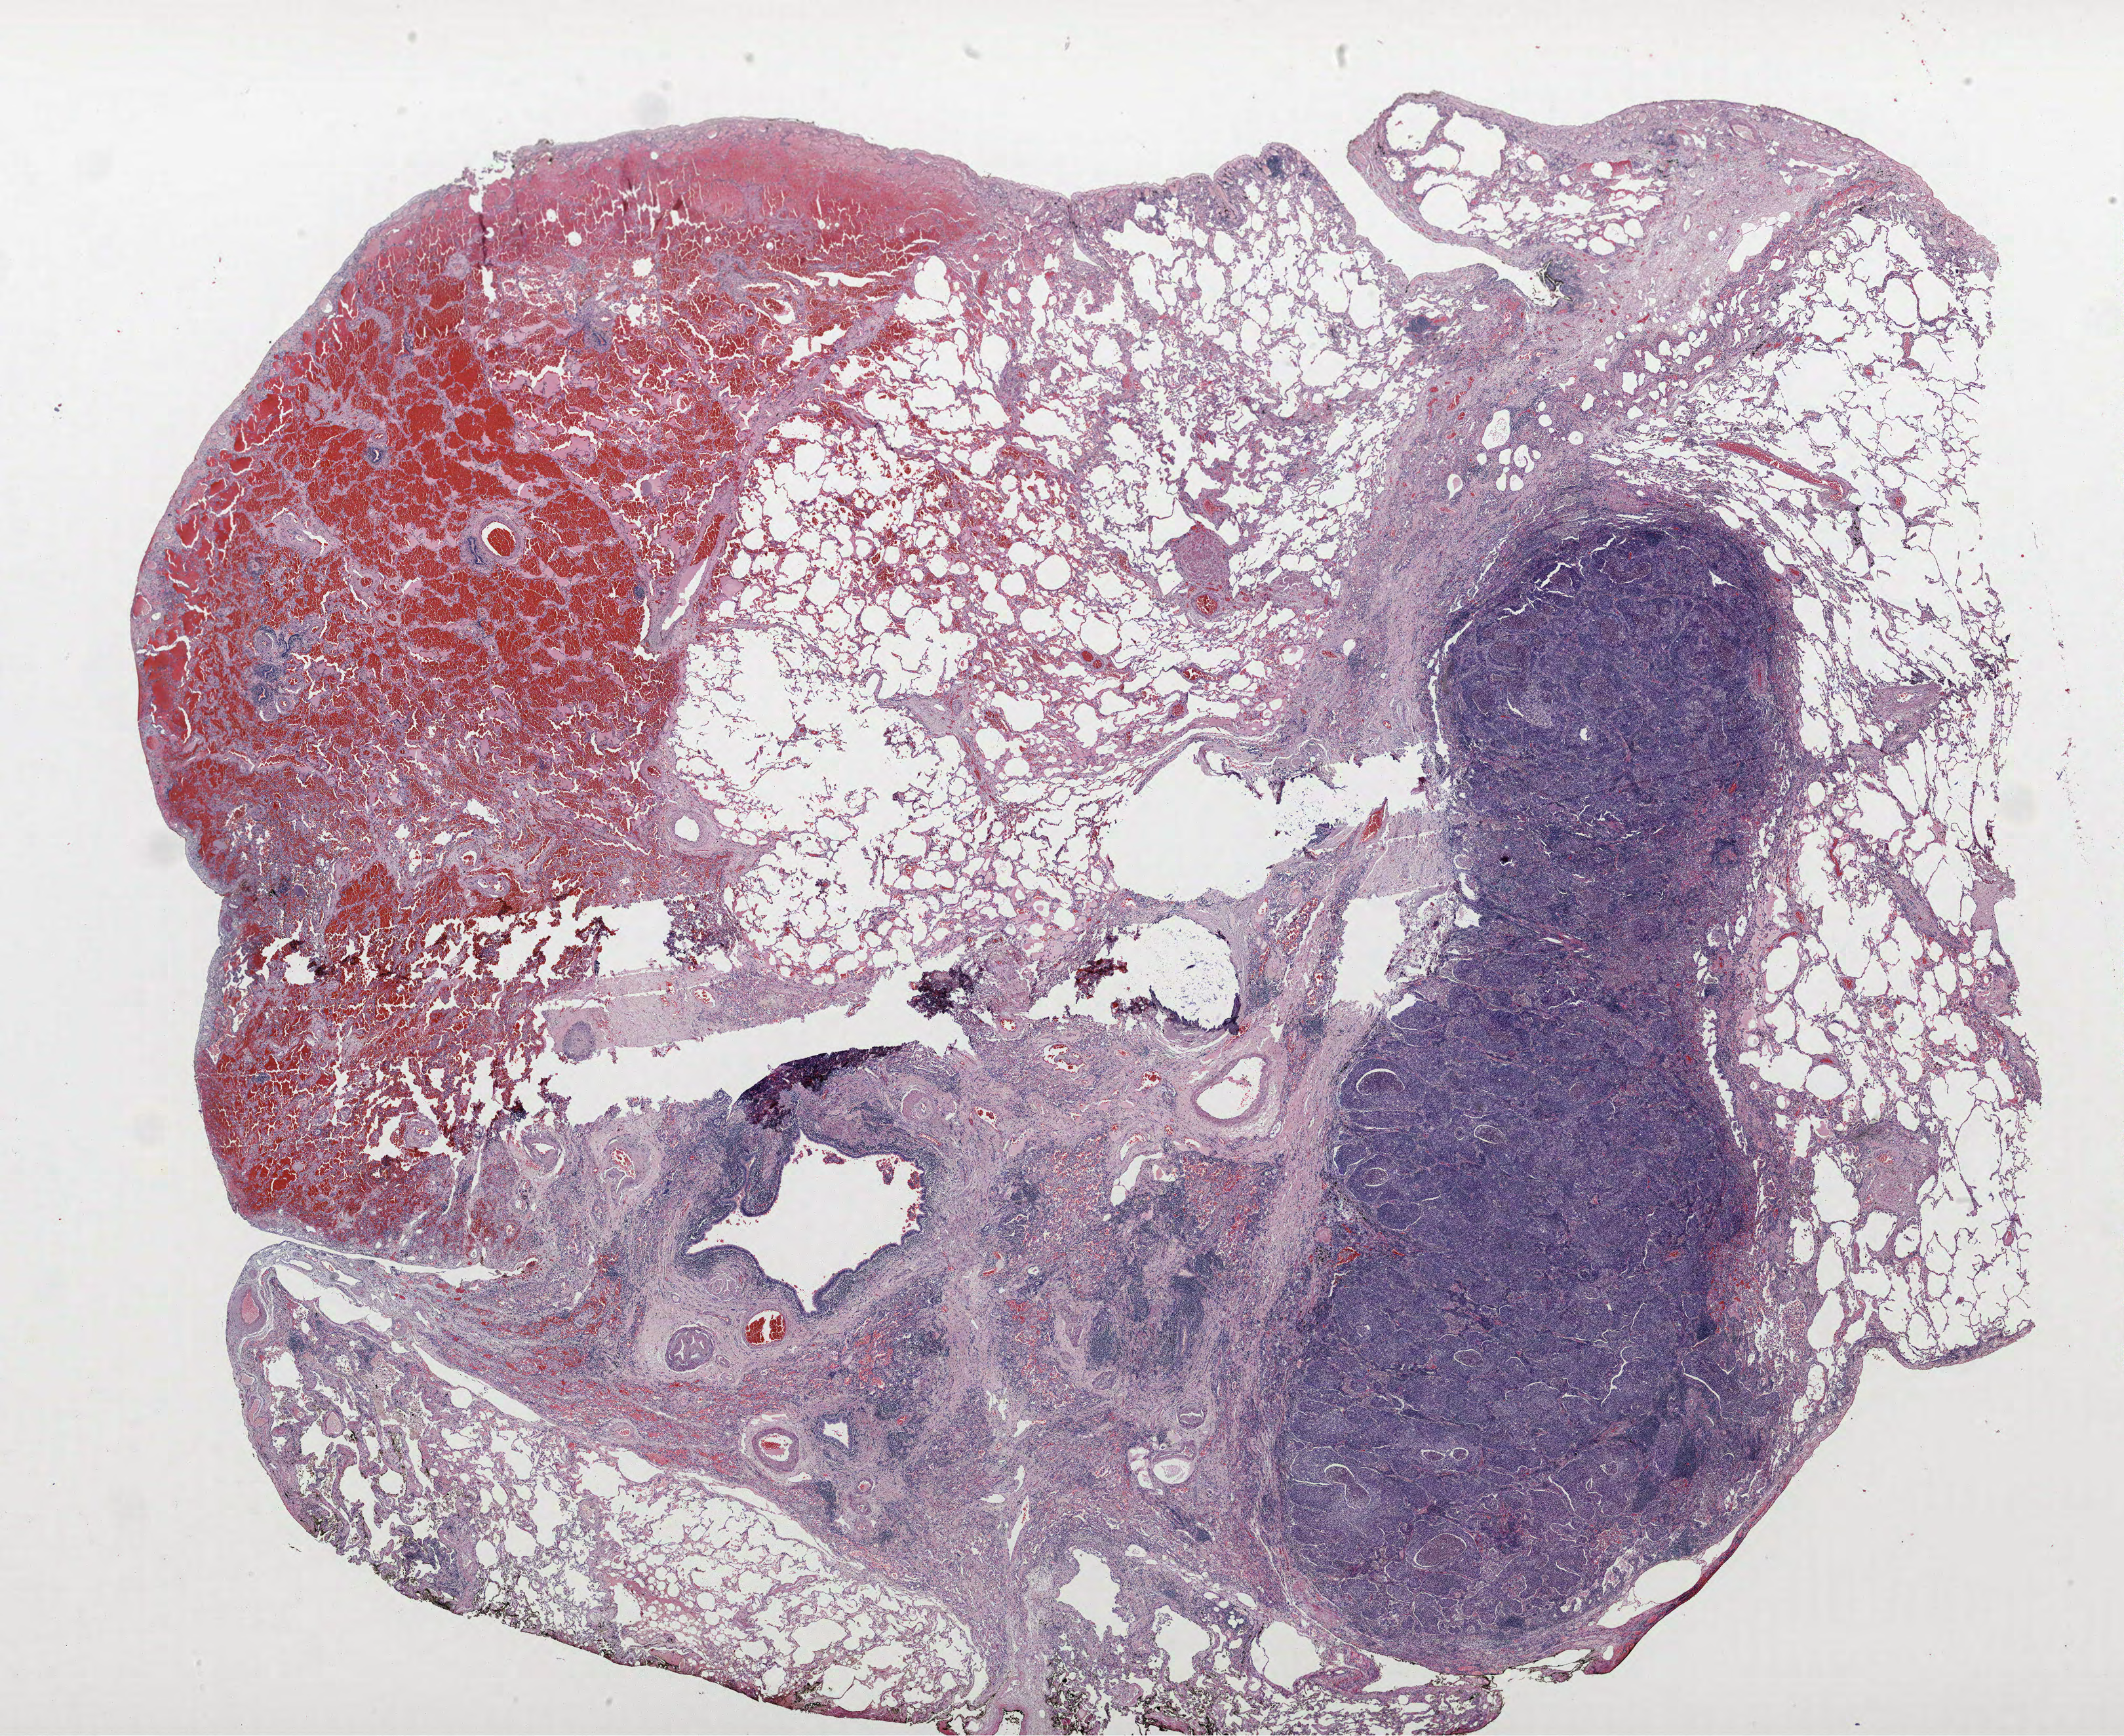
Whole-slide histology image, H&E-stained, a low-resolution overview of the entire scanned area, about 25.9 x 21.2 mm. FFPE section. Lung tissue. Female, age 71 at enrolment. Former smoker at enrolment. Grade: poorly differentiated (G3).
- tumour size (pathology): 30 mm
- participant's lung-cancer diagnosis: Squamous cell carcinoma, NOS
- primary tumour location (clinical record): right upper lobe
- stage (AJCC 6th edition): IA